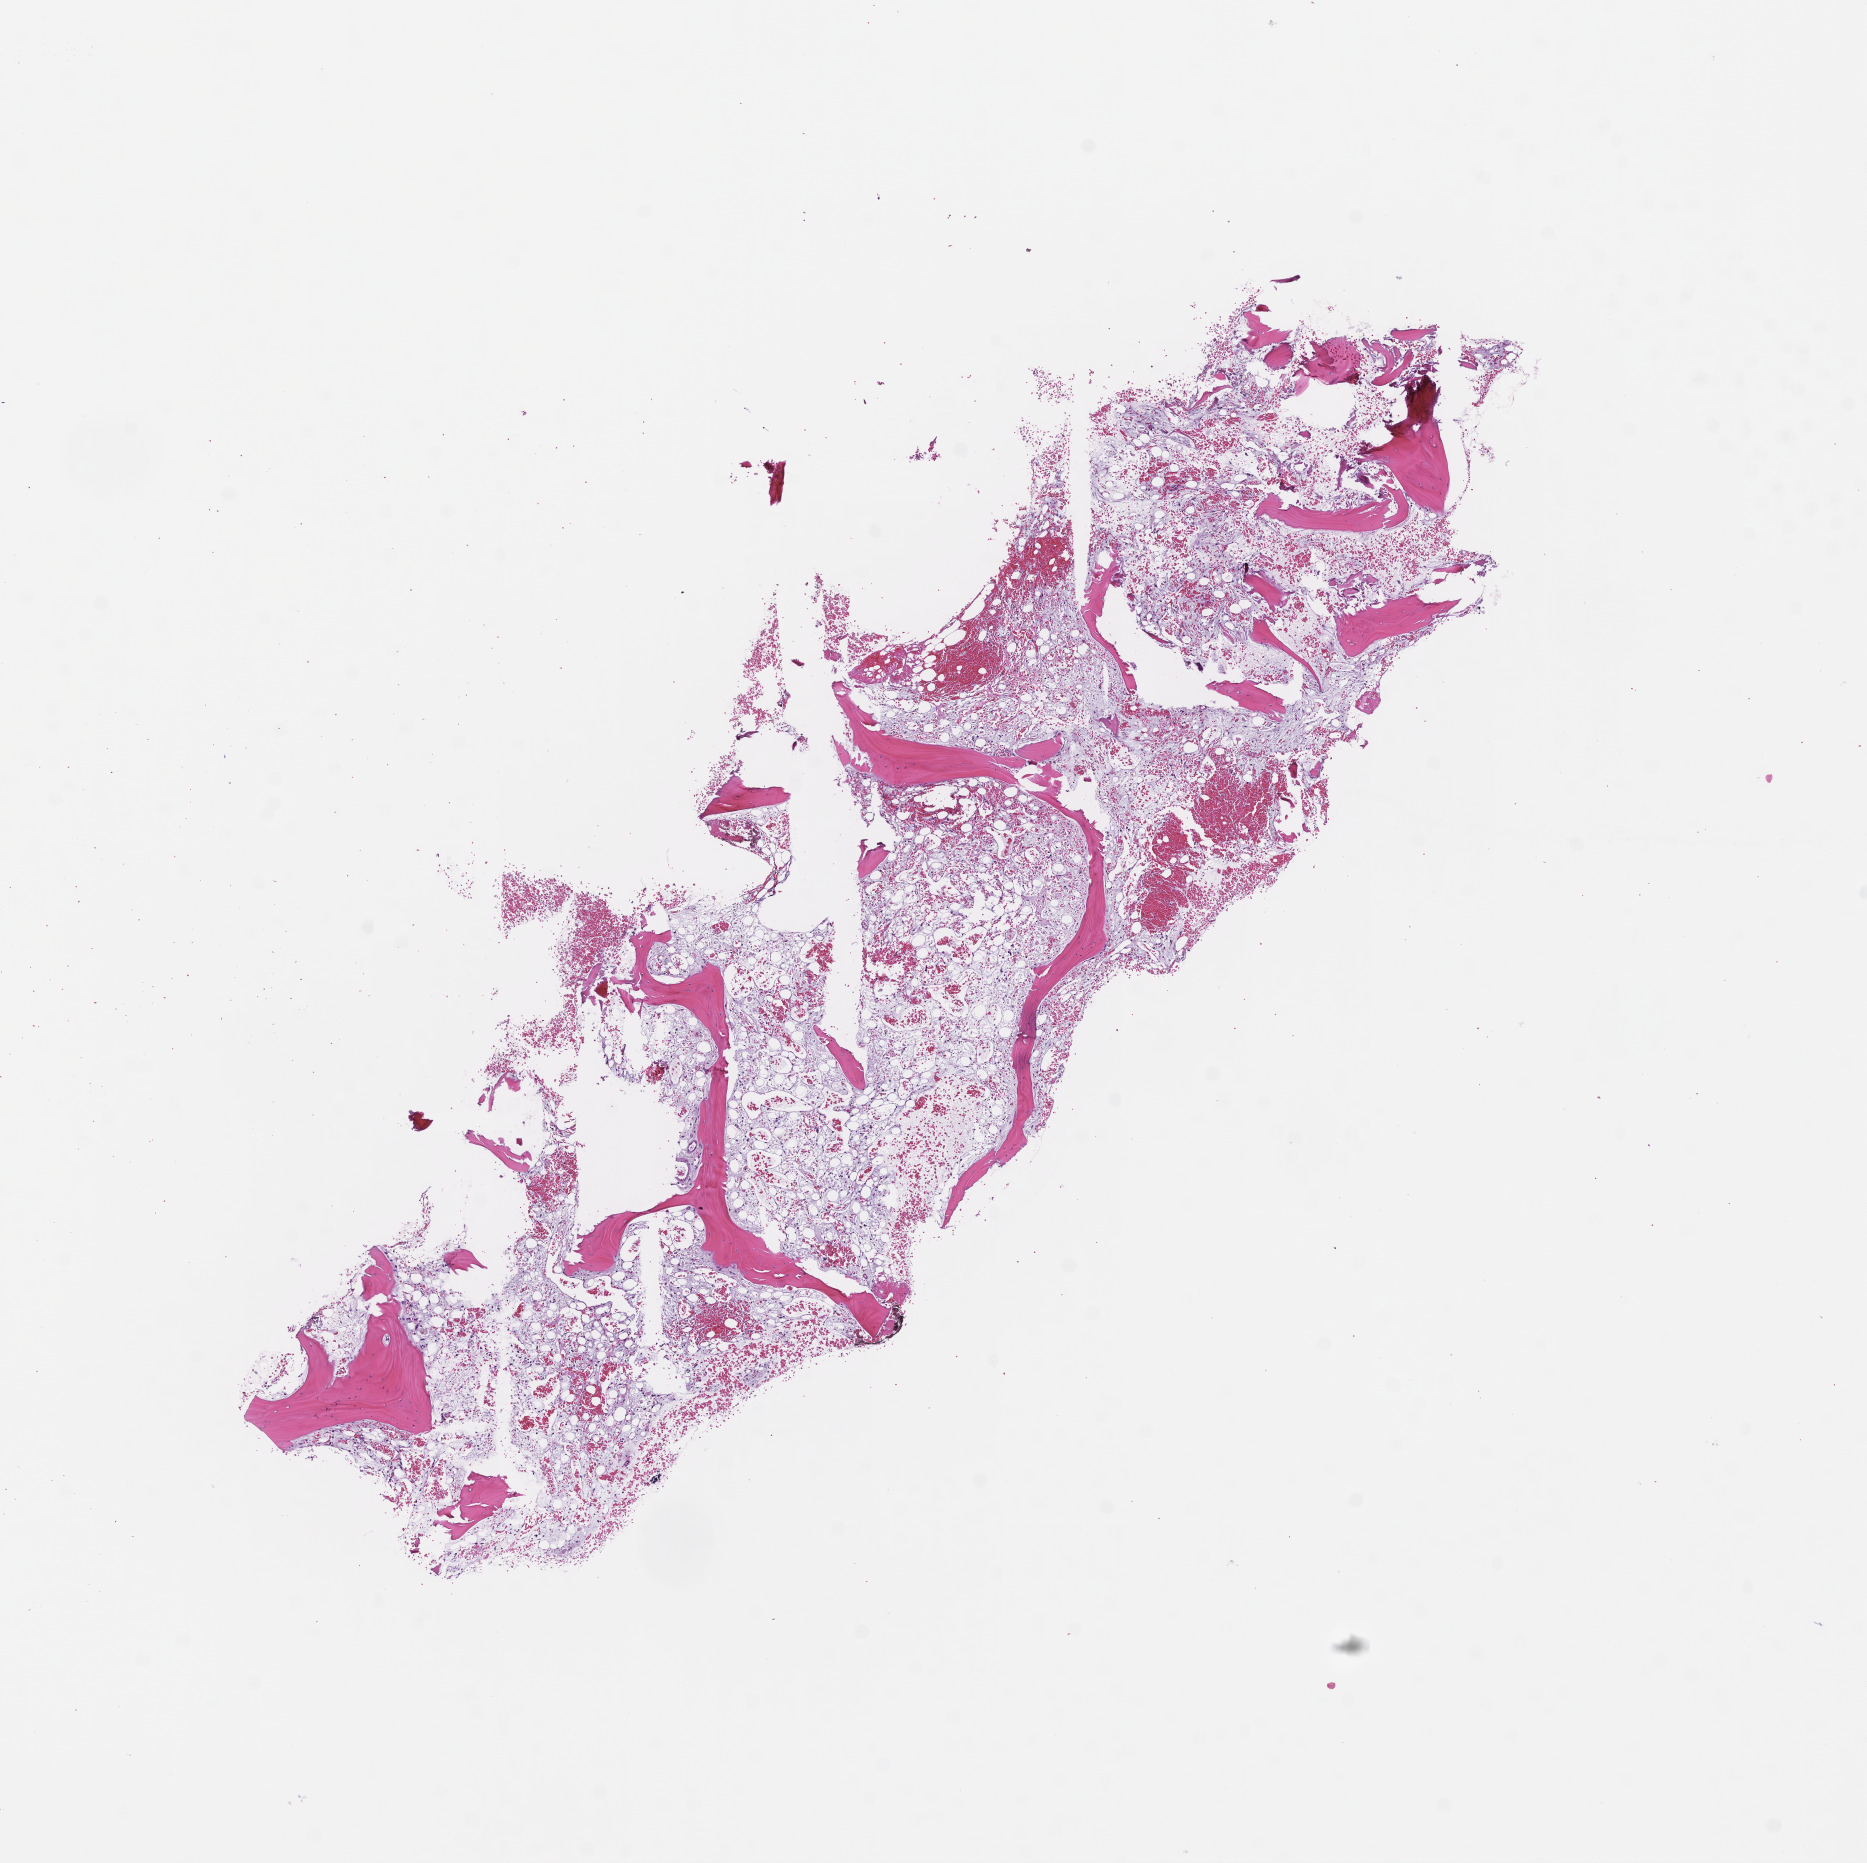
H&E whole-slide image, a low-resolution overview of the entire scanned area, about 7.5 x 7.5 mm; formalin-fixed, paraffin-embedded (FFPE) tissue; site: bone marrow; specimen time point: collected on treatment. Patient sex: female.
This section: primary tumor. Diagnosis: Acute Myeloid Leukemia Not Otherwise Specified.